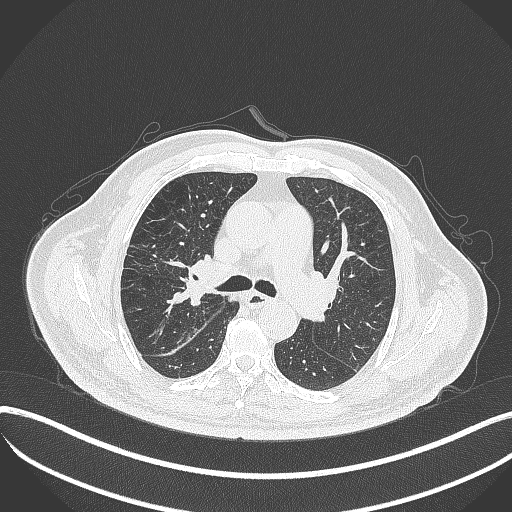
Chest CT, one axial slice. Slice 230 of 401 in the series (ordered by position). Reconstruction kernel B70f. Lung window (W 1500 / L -600 HU). 512 × 512 image matrix, field of view 400 × 400 mm. Patient: male, 72 years. From the clinical record (not read from this slice): clinical TNM (as recorded): T1c N0 M0.
Outlined on this slice (bounding box drawn by a radiologist):
- lung tumour (recorded histology: squamous cell carcinoma): box from (x=176, y=260) to (x=207, y=310) px